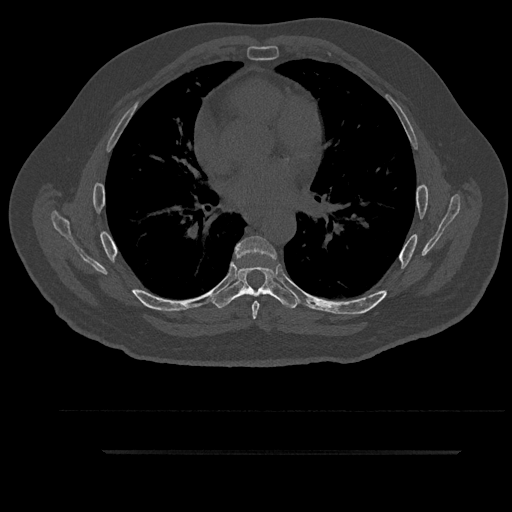
CT including the spine, one axial slice; slice 549 of 797 in the series (ordered by position); reconstruction kernel Br40s/3; 120 kVp; bone window (W 1800 / L 400 HU); 0.5 mm slice thickness; 512 × 512 image matrix, field of view 432 × 432 mm. Patient: male, 63 years. Case-level facts recorded for this patient, not image findings: primary cancer: renal; vertebrae with lytic lesions (as recorded): T8.
Outlined on this slice (semi-automatic segmentation, software-assisted and operator-edited):
- T5 vertebra: bounding box (x1, y1, x2, y2) in pixels: (262, 289, 265, 291)
- T6 vertebra: (235, 236, 276, 319)
- T7 vertebra: (213, 266, 299, 309)